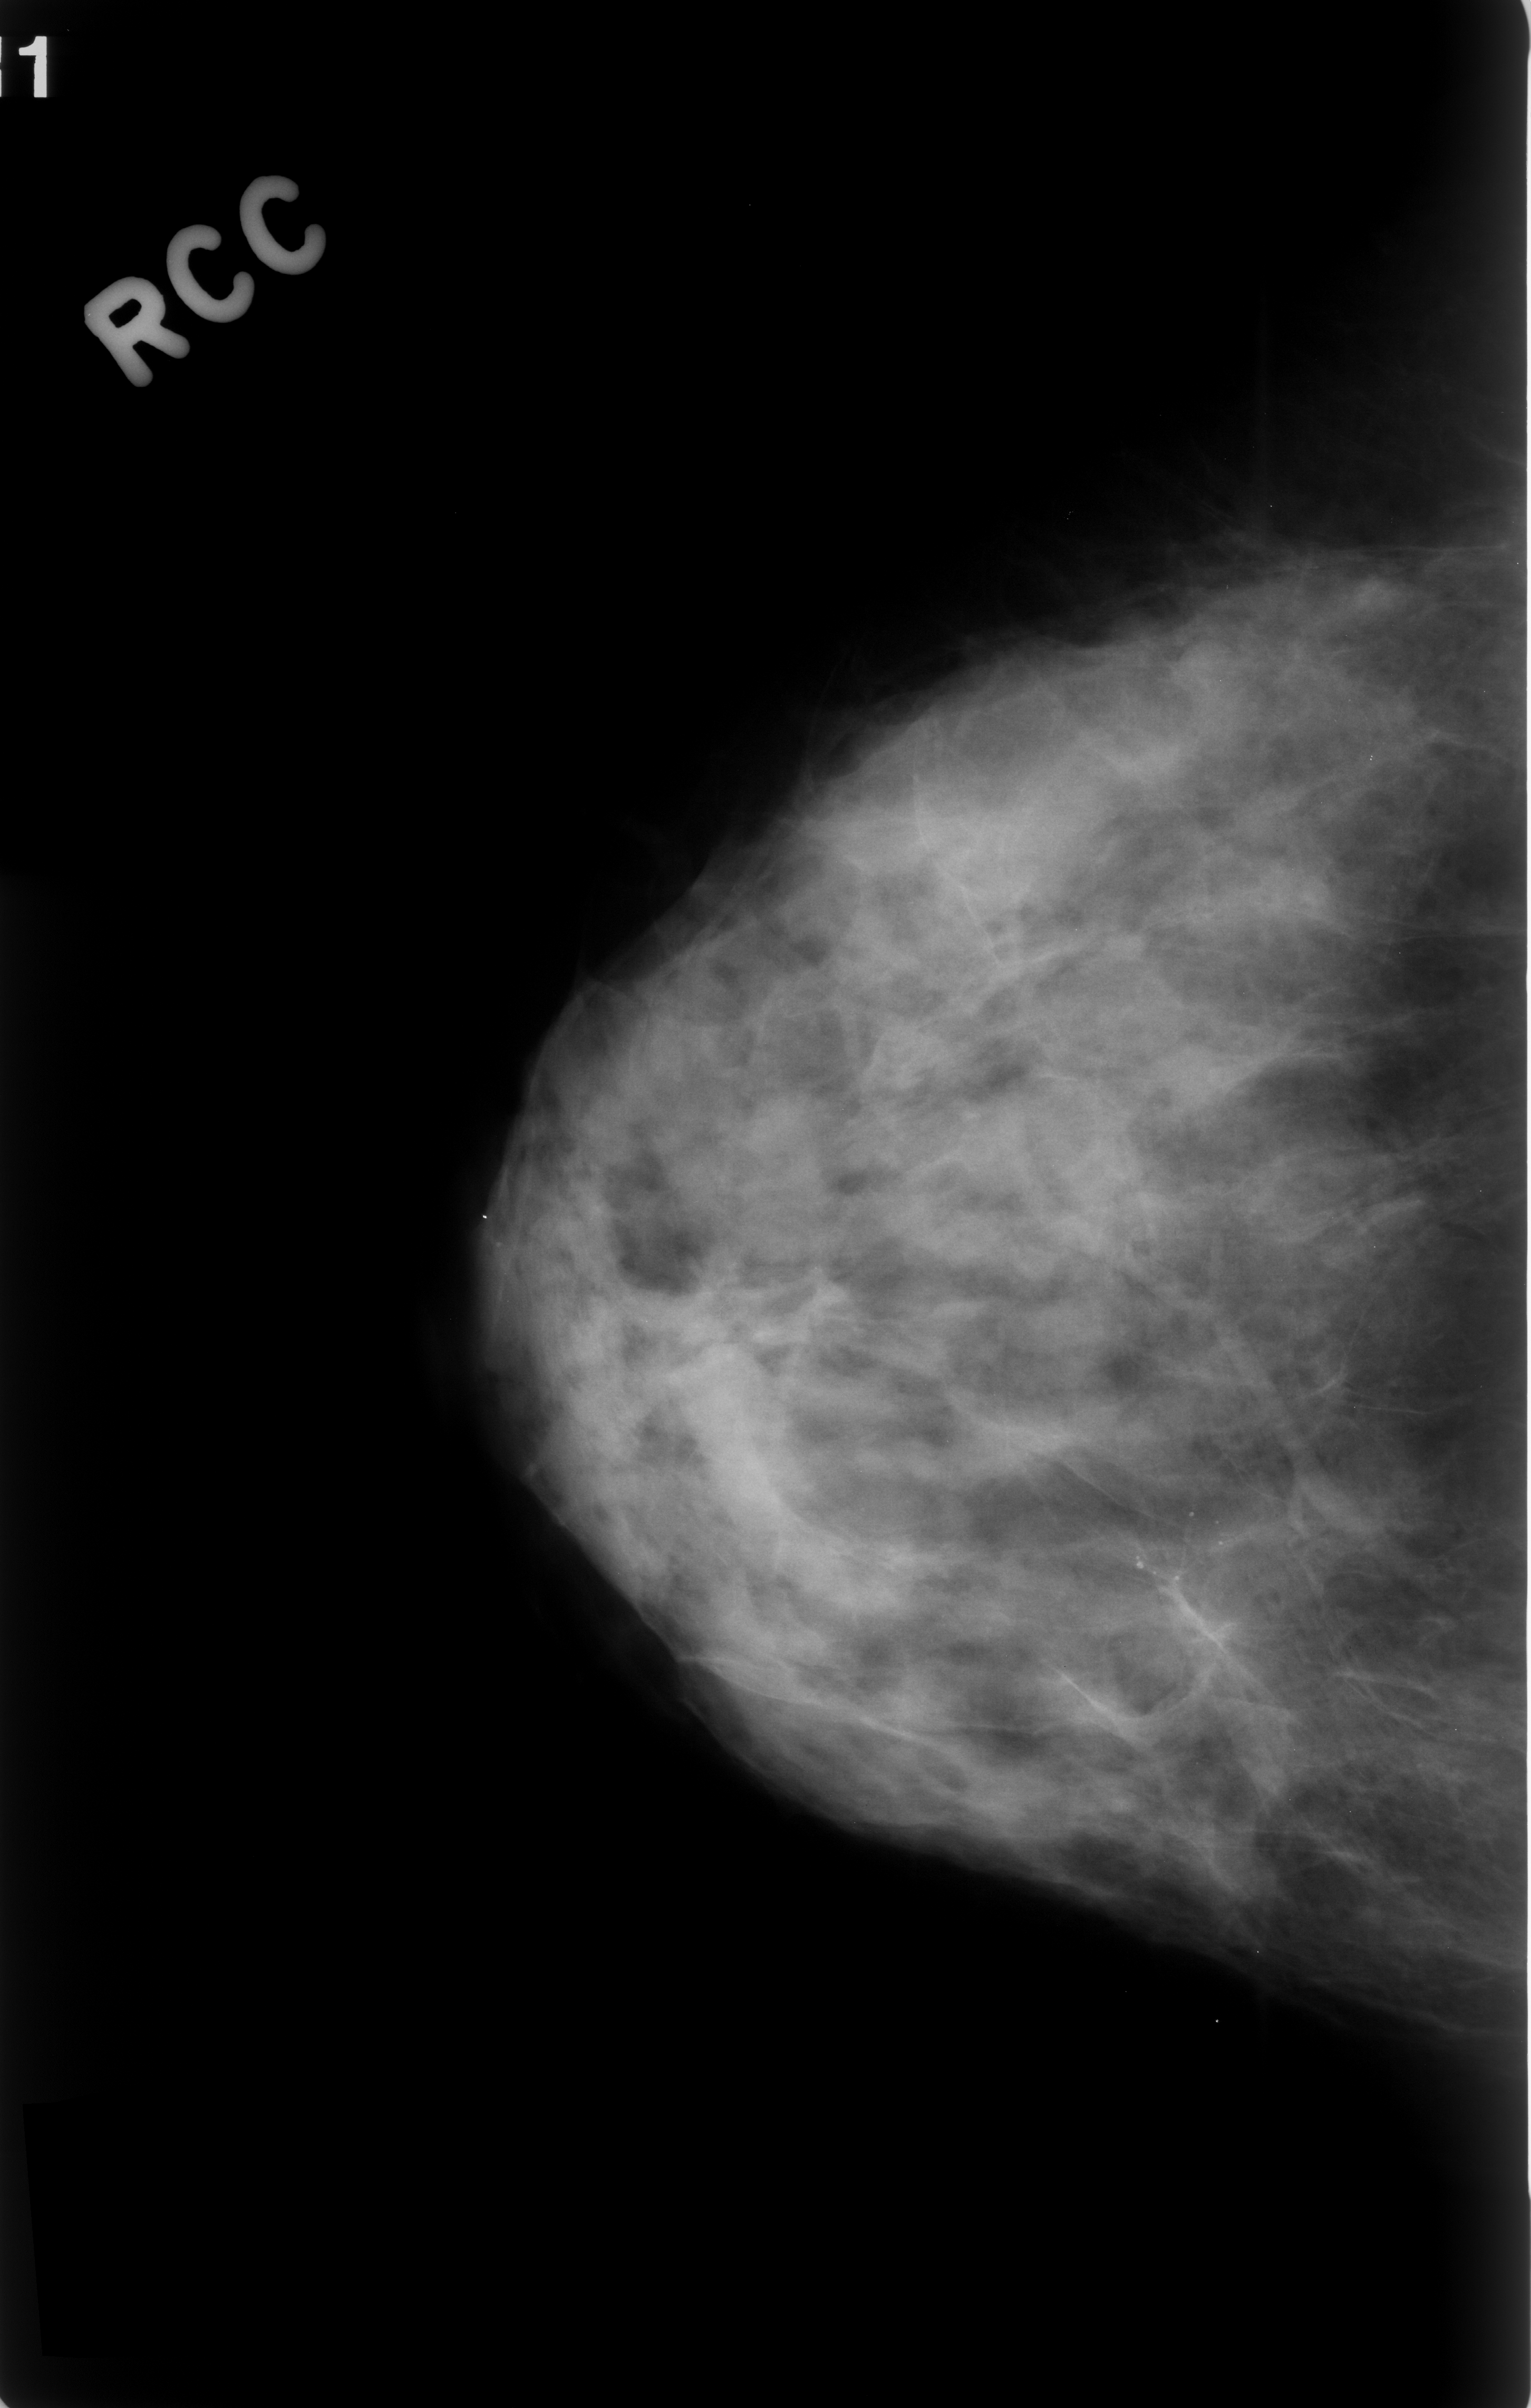
Digitized screen-film mammogram; right breast; craniocaudal (CC) view; BI-RADS breast density category 3 (scale 1–4); 1531 × 2408 image matrix.
Marked abnormalities (boxes around the expert regions of interest):
- calcifications, morphology round and regular, distribution clustered; BI-RADS assessment category 4; subtlety rating 4 on a 1 (subtle) to 5 (obvious) scale; pathology (as recorded): benign: bounding box <1071,1492,1325,1722> (left, top, right, bottom; pixels)